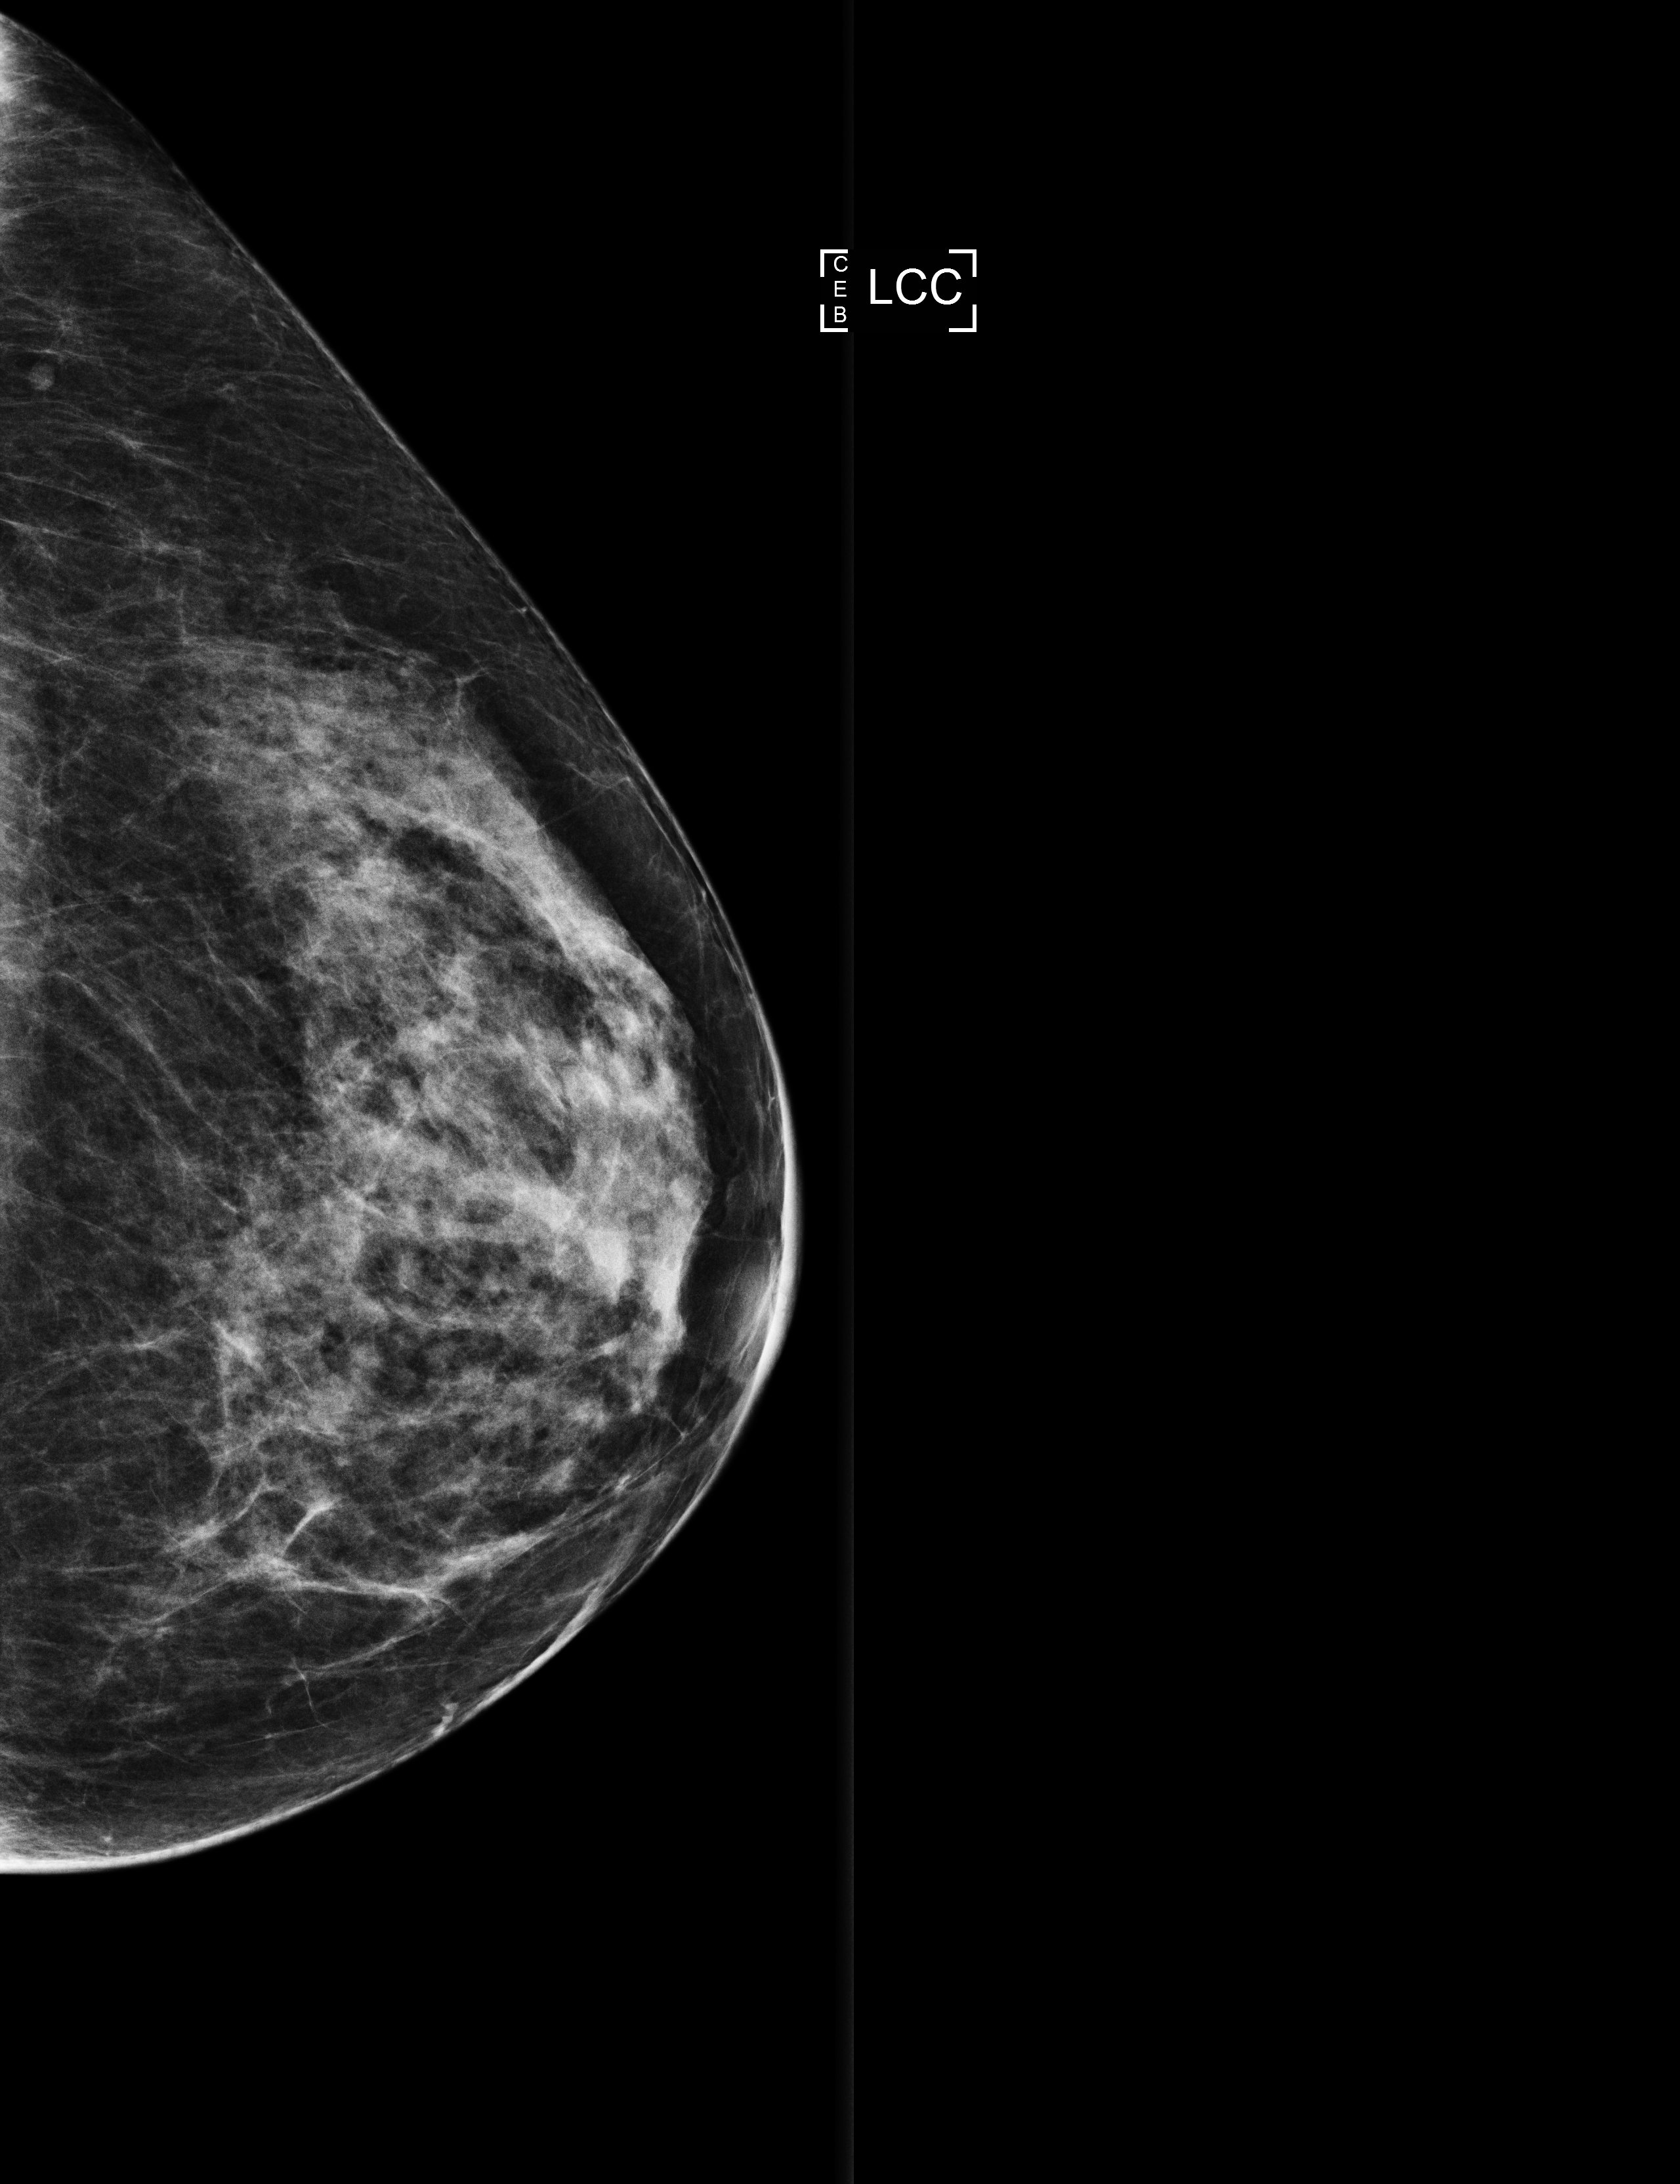
Digital mammogram (FFDM); left breast; craniocaudal (CC) view; annual screening mammography examination. Female patient, age 68 years.
- BI-RADS breast density category at the screening exam (both breasts, scale 1–4): 3
- final BI-RADS category for the screening round (tomosynthesis exam, both breasts): category 2
- recall: no recall after this screen